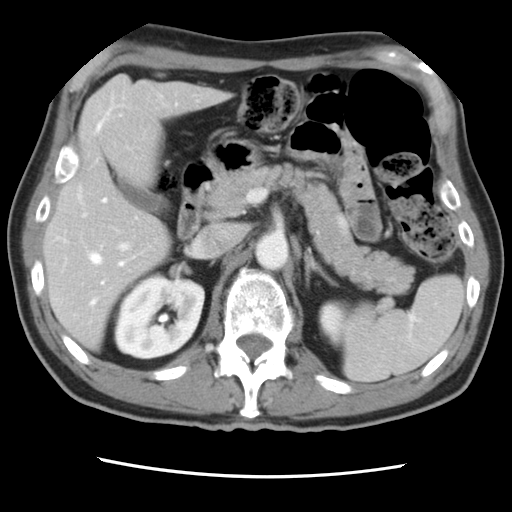
Contrast-enhanced abdominal CT, one axial slice. Slice 45 of 83 in the series (ordered by position). Intravenous contrast given. Soft-tissue window (W 400 / L 40 HU). 5 mm slice thickness. 512 × 512 image matrix, field of view 321 × 321 mm. Male patient, age 69 years. Case-level facts recorded for this patient, not image findings: diagnosis: colorectal cancer liver metastases, imaged before liver resection; multiple liver metastases: yes; largest metastasis: 3.5 cm; disease in both lobes: no.
Structures marked on this image (manually delineated by an expert):
- hepatic veins: bounding box (x1, y1, x2, y2) in pixels: (89, 104, 177, 305)
- liver: (45, 77, 225, 347)
- planned liver remnant (the part of the liver to remain after resection): (45, 144, 172, 347)
- portal vein (with intrahepatic branches): (65, 186, 130, 264)